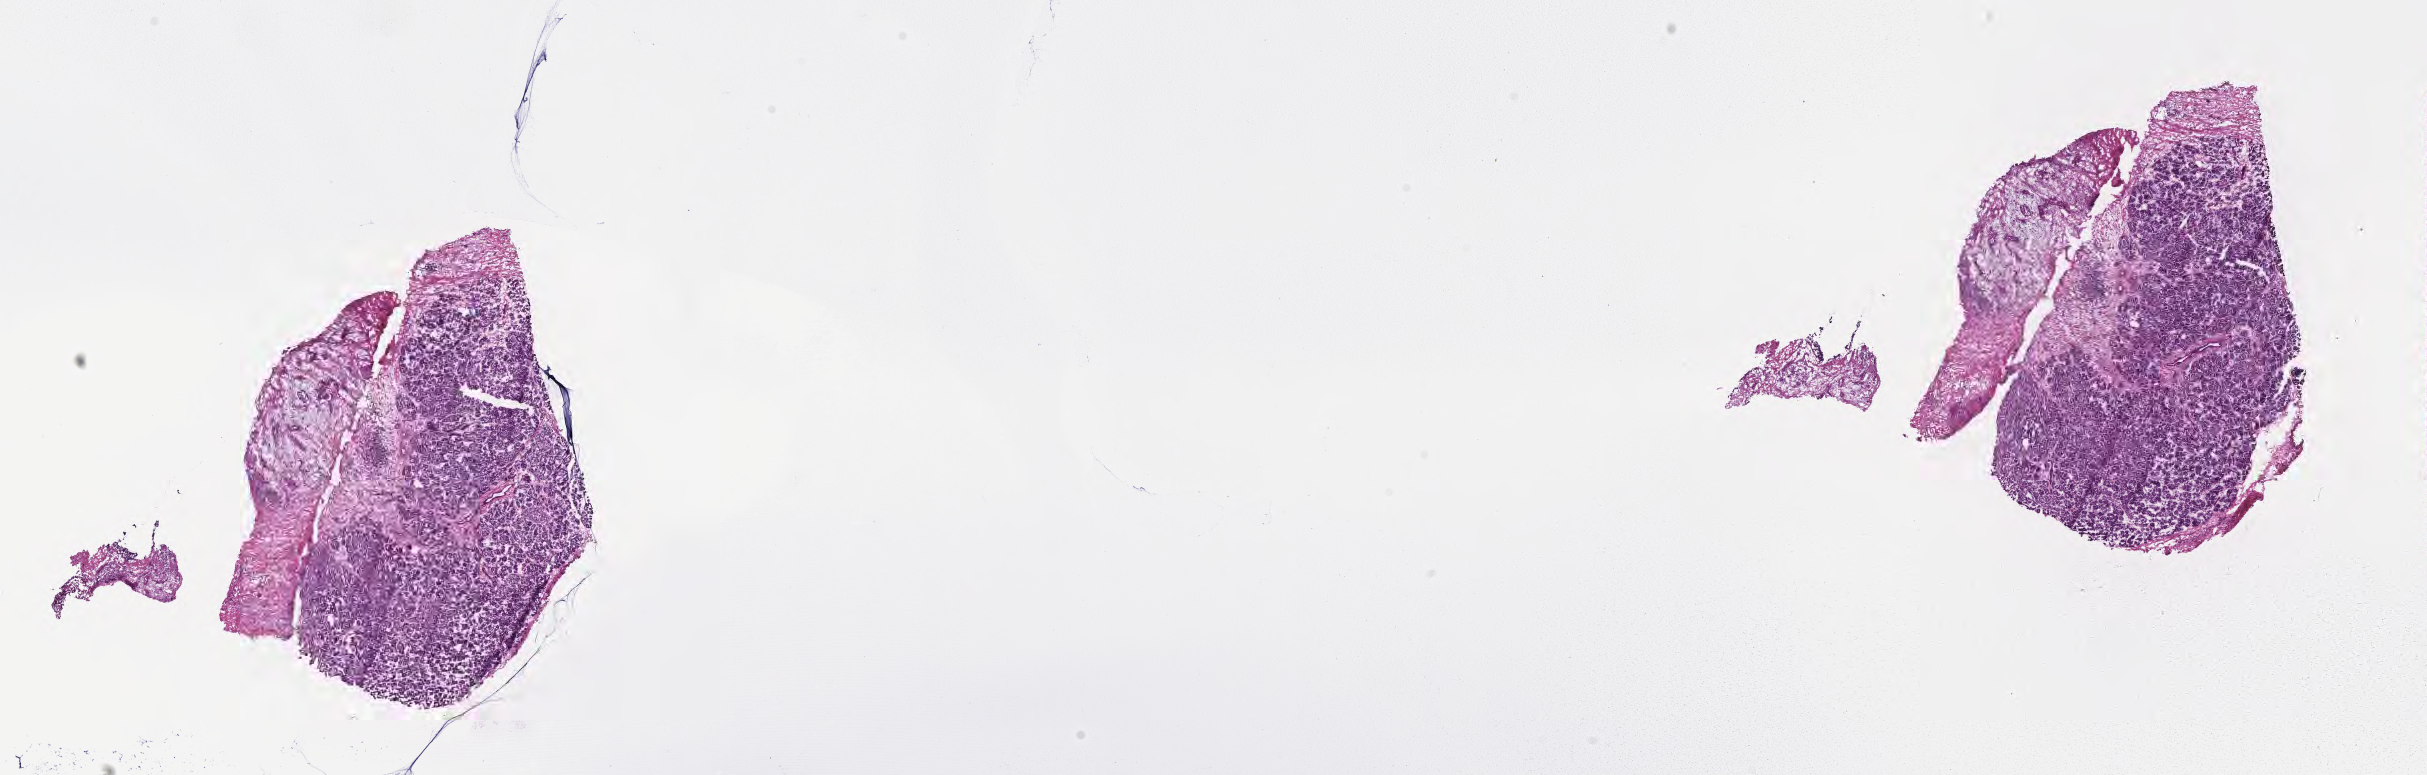
H&E whole-slide image — low-resolution overview of the scanned area, about 19.6 x 6.3 mm, cryosection, primary tumor, site: head of pancreas. Female patient; age at initial diagnosis 71 years. Tumor grade: G3 (poorly differentiated). Pathologist review of this section (percent, as recorded): tumor cells 62%, tumor nuclei 75%, stromal cells 38%, necrosis 0%, normal cells 0%. Infiltration values recorded for this section: lymphocyte infiltration 20%, monocyte infiltration 1%, neutrophil infiltration 0%.
* section: bottom of the tissue portion
* diagnosis: Infiltrating duct carcinoma, NOS
* AJCC pathologic stage: Stage III